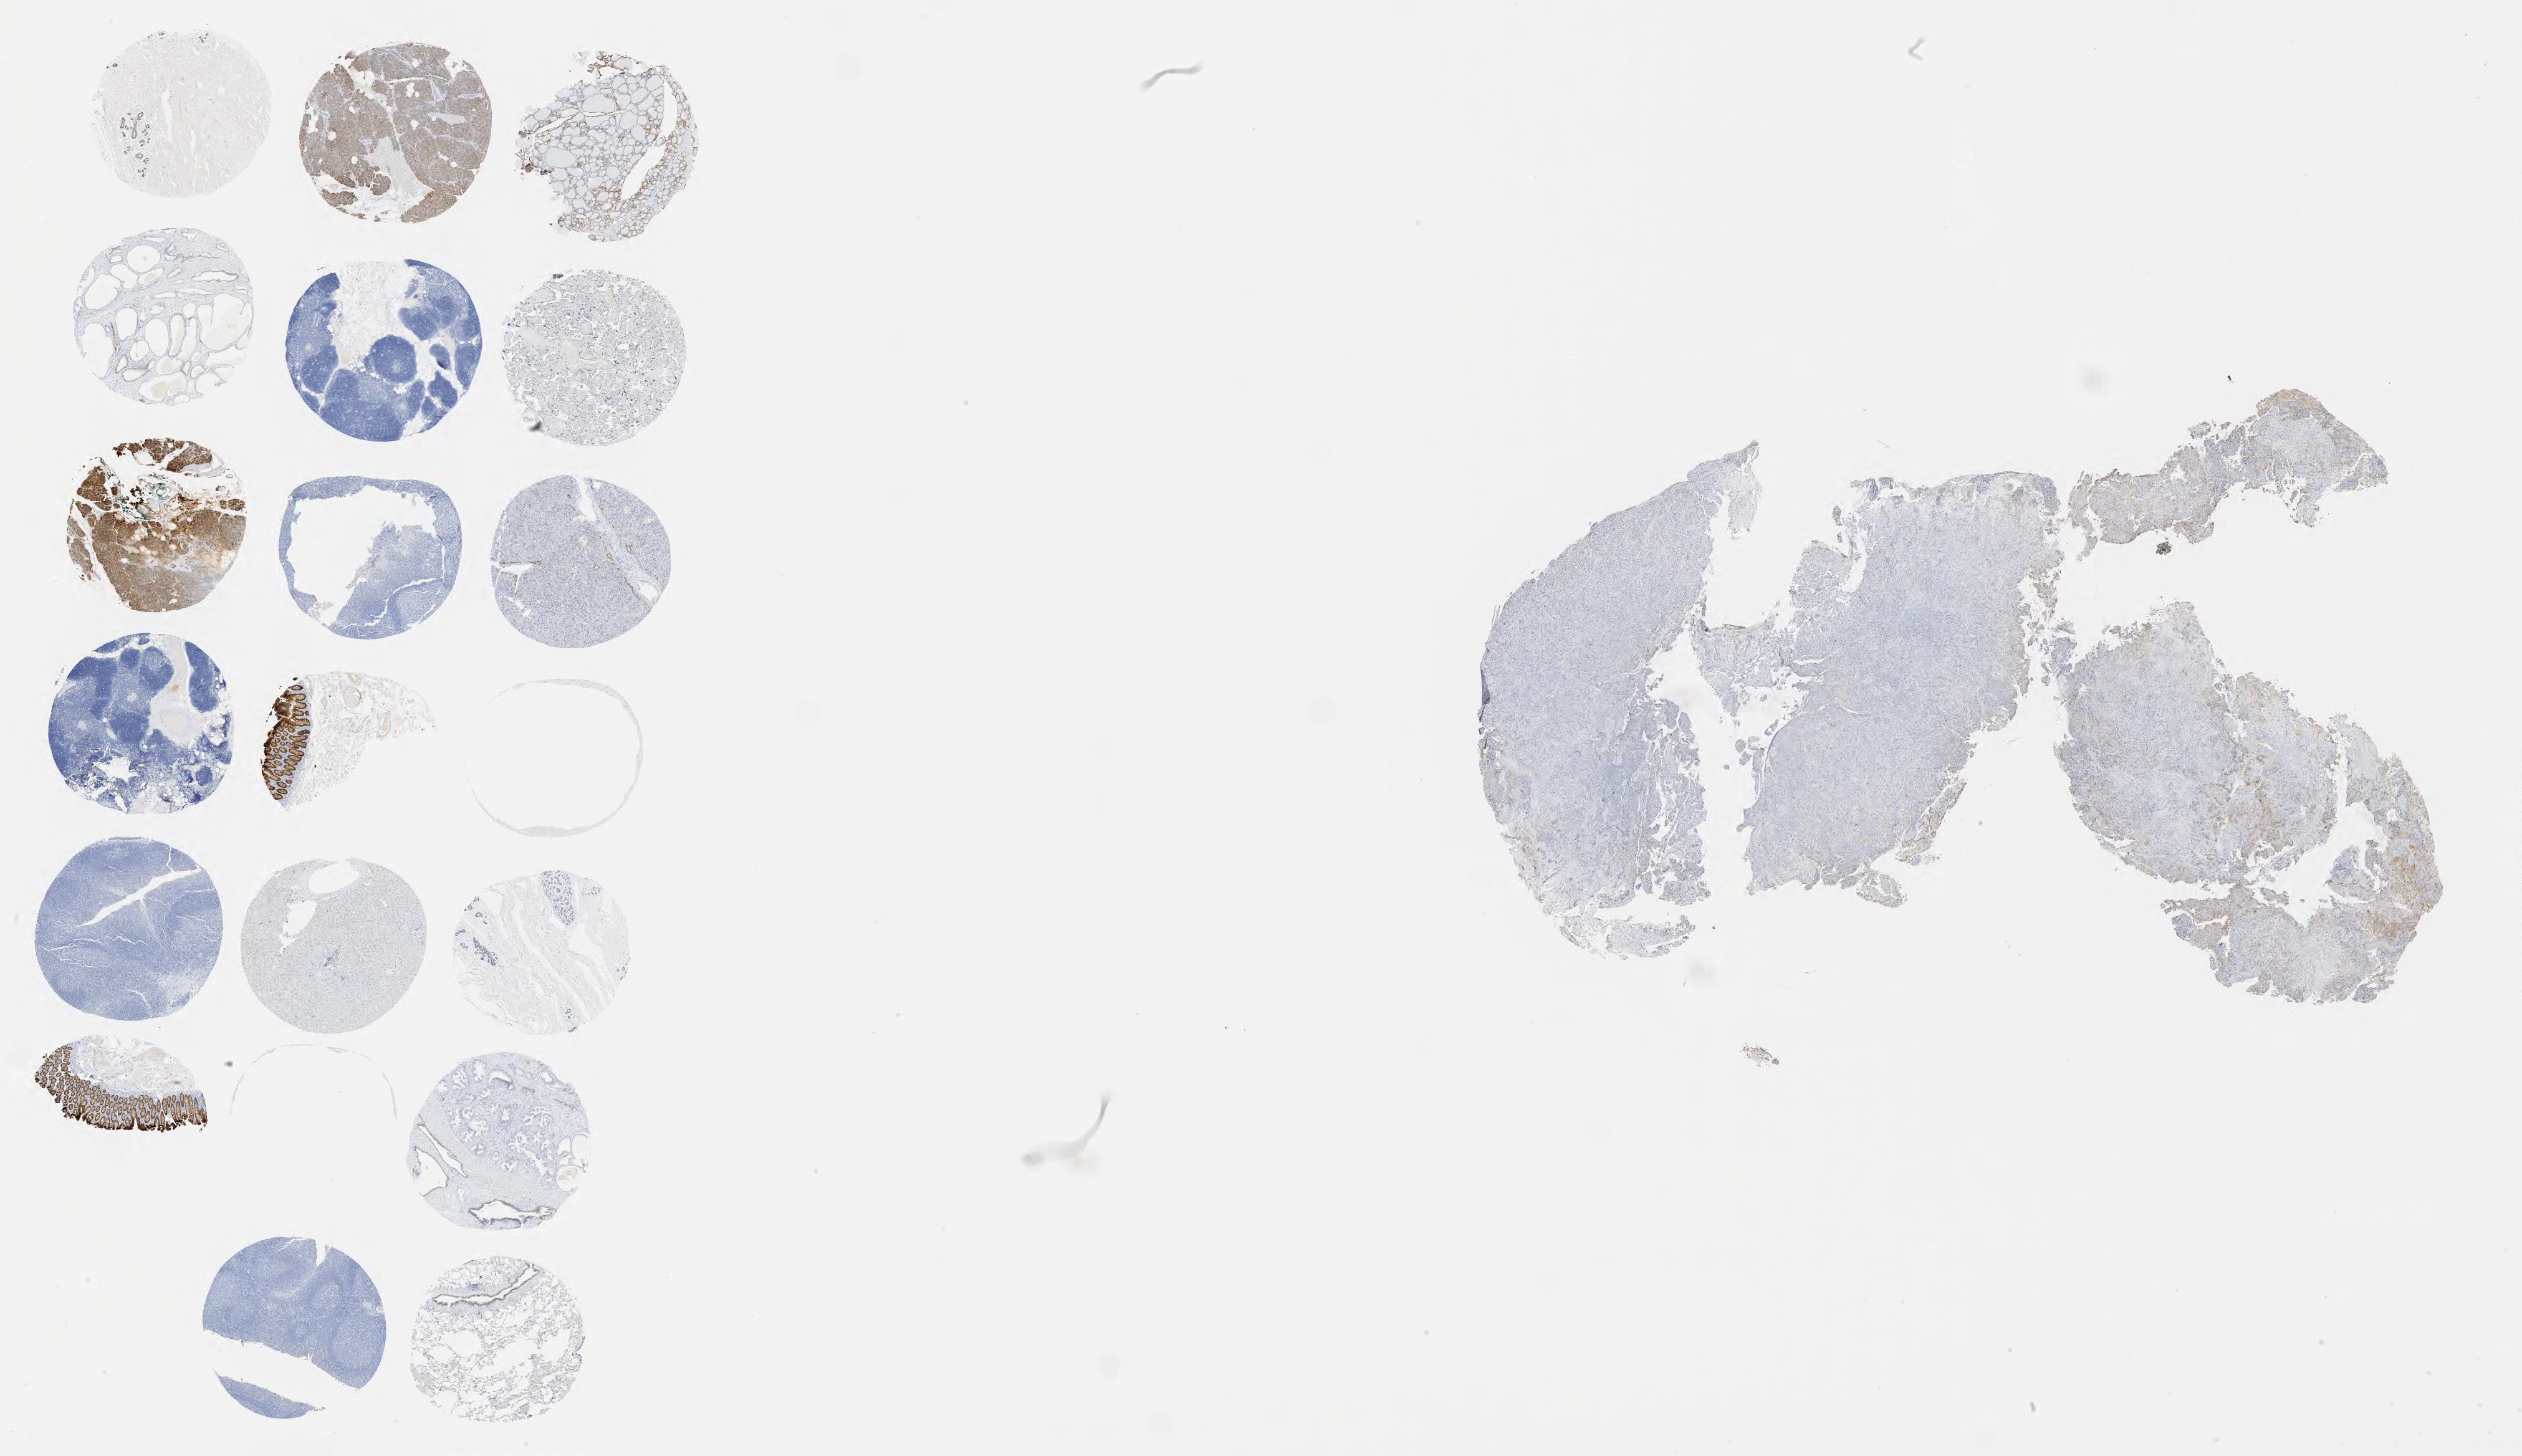
IHC for Ber-EP4, whole-slide image — low-resolution overview of the scanned area, about 32.7 x 18.9 mm; tumor tissue; site: cervix. Female patient, 54 years old.
- diagnosis: Adenocarcinoma, NOS